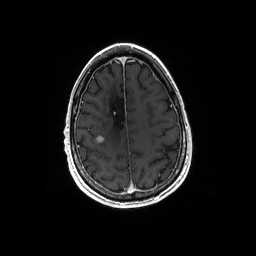
Brain MRI from a brain-tumour surgery series, one axial slice. Position 49 of 192 along the scan axis. T1-weighted post-contrast. 1 mm slice thickness. 256 × 256 image matrix, field of view 256 × 256 mm. From the clinical record (not read from this slice): histopathology: Astrocytoma; WHO grade: 4; IDH mutation: yes; tumour location: Right Frontal.
Structures marked on this image (expert manual segmentation):
- tumour: bounding box [x1, y1, x2, y2] px = [95, 137, 104, 144]